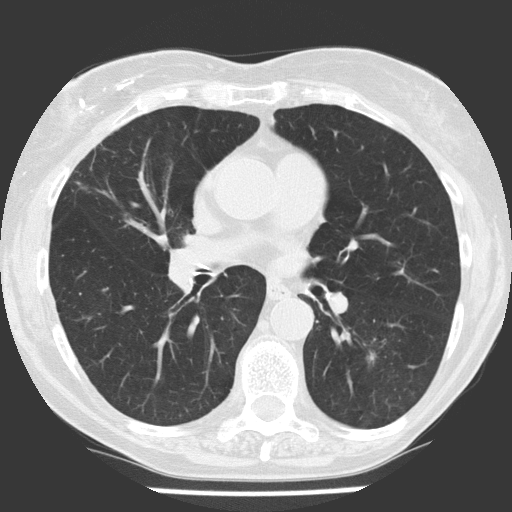
Chest CT (low-dose screening protocol), one axial image. Baseline annual screen. Lung window (W 1500 / L -600 HU). 2 mm slice thickness. Lung (sharp) reconstruction kernel (FC51). Slice 71 of 147 in the series. 512 × 512 image matrix, field of view 290 × 290 mm. Female, age 68 years at enrolment. Former smoker at enrolment.
Lesion marked by an expert reader, bounding box (x1, y1, x2, y2) in pixels: (348, 326, 398, 379). Screening reader's record for this exam: no non-calcified nodule ≥4 mm recorded. Lung cancer was diagnosed 895 days after this screen (after the third annual screen): non-small cell carcinoma, left lower lobe, poorly differentiated (G3), stage IA (AJCC 6th edition), 10 mm at pathology.